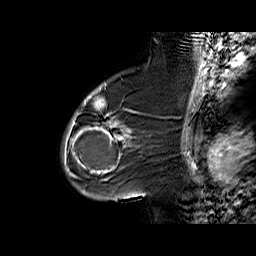
Breast MRI (dynamic contrast-enhanced), one sagittal slice; position 42 of 60 along the scan axis; dynamic contrast-enhanced series, time point 2 of 6 at this slice position (early post-contrast); 1.5 T; TE 6.3 ms, TR 32.4 ms; 4 mm slice thickness; 256 × 256 image matrix, field of view 200 × 200 mm. Female patient. Case-level facts recorded for this patient, not image findings: setting: breast cancer imaged before/during neoadjuvant chemotherapy; receptor status: triple-negative.
Structures marked on this image (semi-automatically segmented with operator editing):
- analysis volume of interest (the breast-tissue region the enhancement analysis was run in; not a lesion): bounding box (x1, y1, x2, y2) in pixels: (65, 88, 142, 187)
- tumour enhancement mask (voxels above the 100 % enhancement threshold inside the analysis volume of interest): (65, 89, 131, 174)